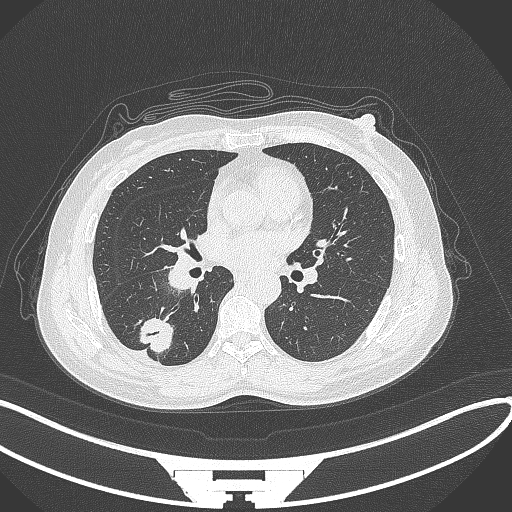
Chest CT, one axial slice; slice 150 of 352 in the series (ordered by position); lung window (W 1500 / L -600 HU); 1 mm slice thickness; 512 × 512 image matrix, field of view 400 × 400 mm. Female patient, age 55 years. Case-level facts recorded for this patient, not image findings: clinical TNM (as recorded): T1c N1 M0.
Structures marked on this image (bounding box drawn by a radiologist):
- lung tumour (recorded histology: adenocarcinoma): box from (x=135, y=313) to (x=177, y=356) px